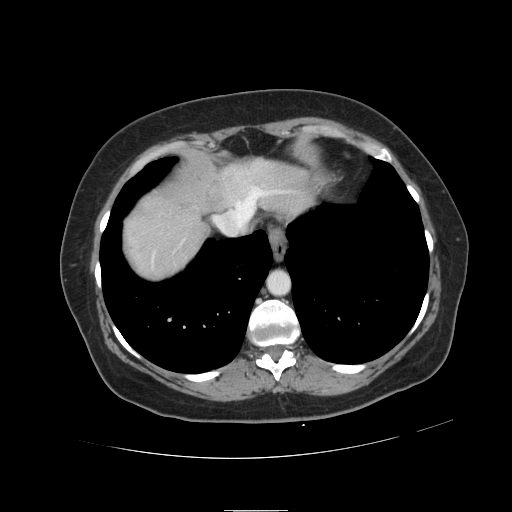
Contrast-enhanced abdominal CT, one axial slice. Position 107 of 121 along the scan axis. Intravenous contrast given. Soft-tissue window (W 400 / L 40 HU). 2.5 mm slice thickness. 512 × 512 image matrix. Female patient, age 52 years. From the clinical record (not read from this slice): diagnosis: colorectal cancer liver metastases, imaged before liver resection; multiple liver metastases: yes; largest metastasis: 6.3 cm; disease in both lobes: no.
Structures marked on this image (manually delineated by an expert):
- hepatic veins: box from (x=152, y=186) to (x=272, y=264) px
- liver: (x=123, y=161)–(x=313, y=281)
- planned liver remnant (the part of the liver to remain after resection): (x=200, y=160)–(x=313, y=211)